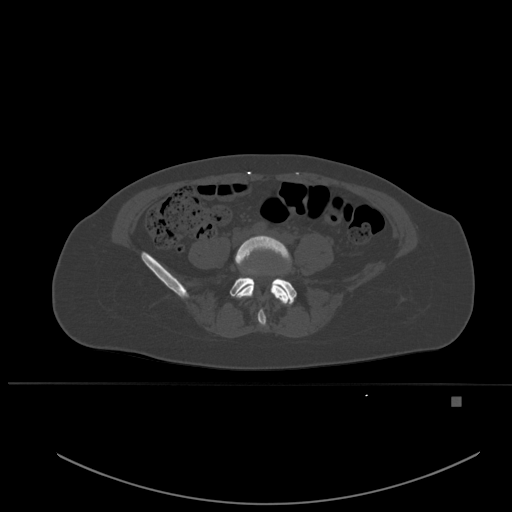
CT including the spine, one axial slice. Position 163 of 651 along the scan axis. Bone window (W 1800 / L 400 HU). 1.5 mm slice thickness. 512 × 512 image matrix, field of view 443 × 443 mm. Female patient, age 49 years. Case-level facts recorded for this patient, not image findings: primary cancer: breast; vertebrae with lytic lesions (as recorded): L3, T12, L4.
Annotated regions visible in this slice (semi-automatically segmented with operator editing):
- L4 vertebra: bounding box [x1, y1, x2, y2] px = [235, 235, 291, 326]
- L5 vertebra: [230, 260, 297, 304]